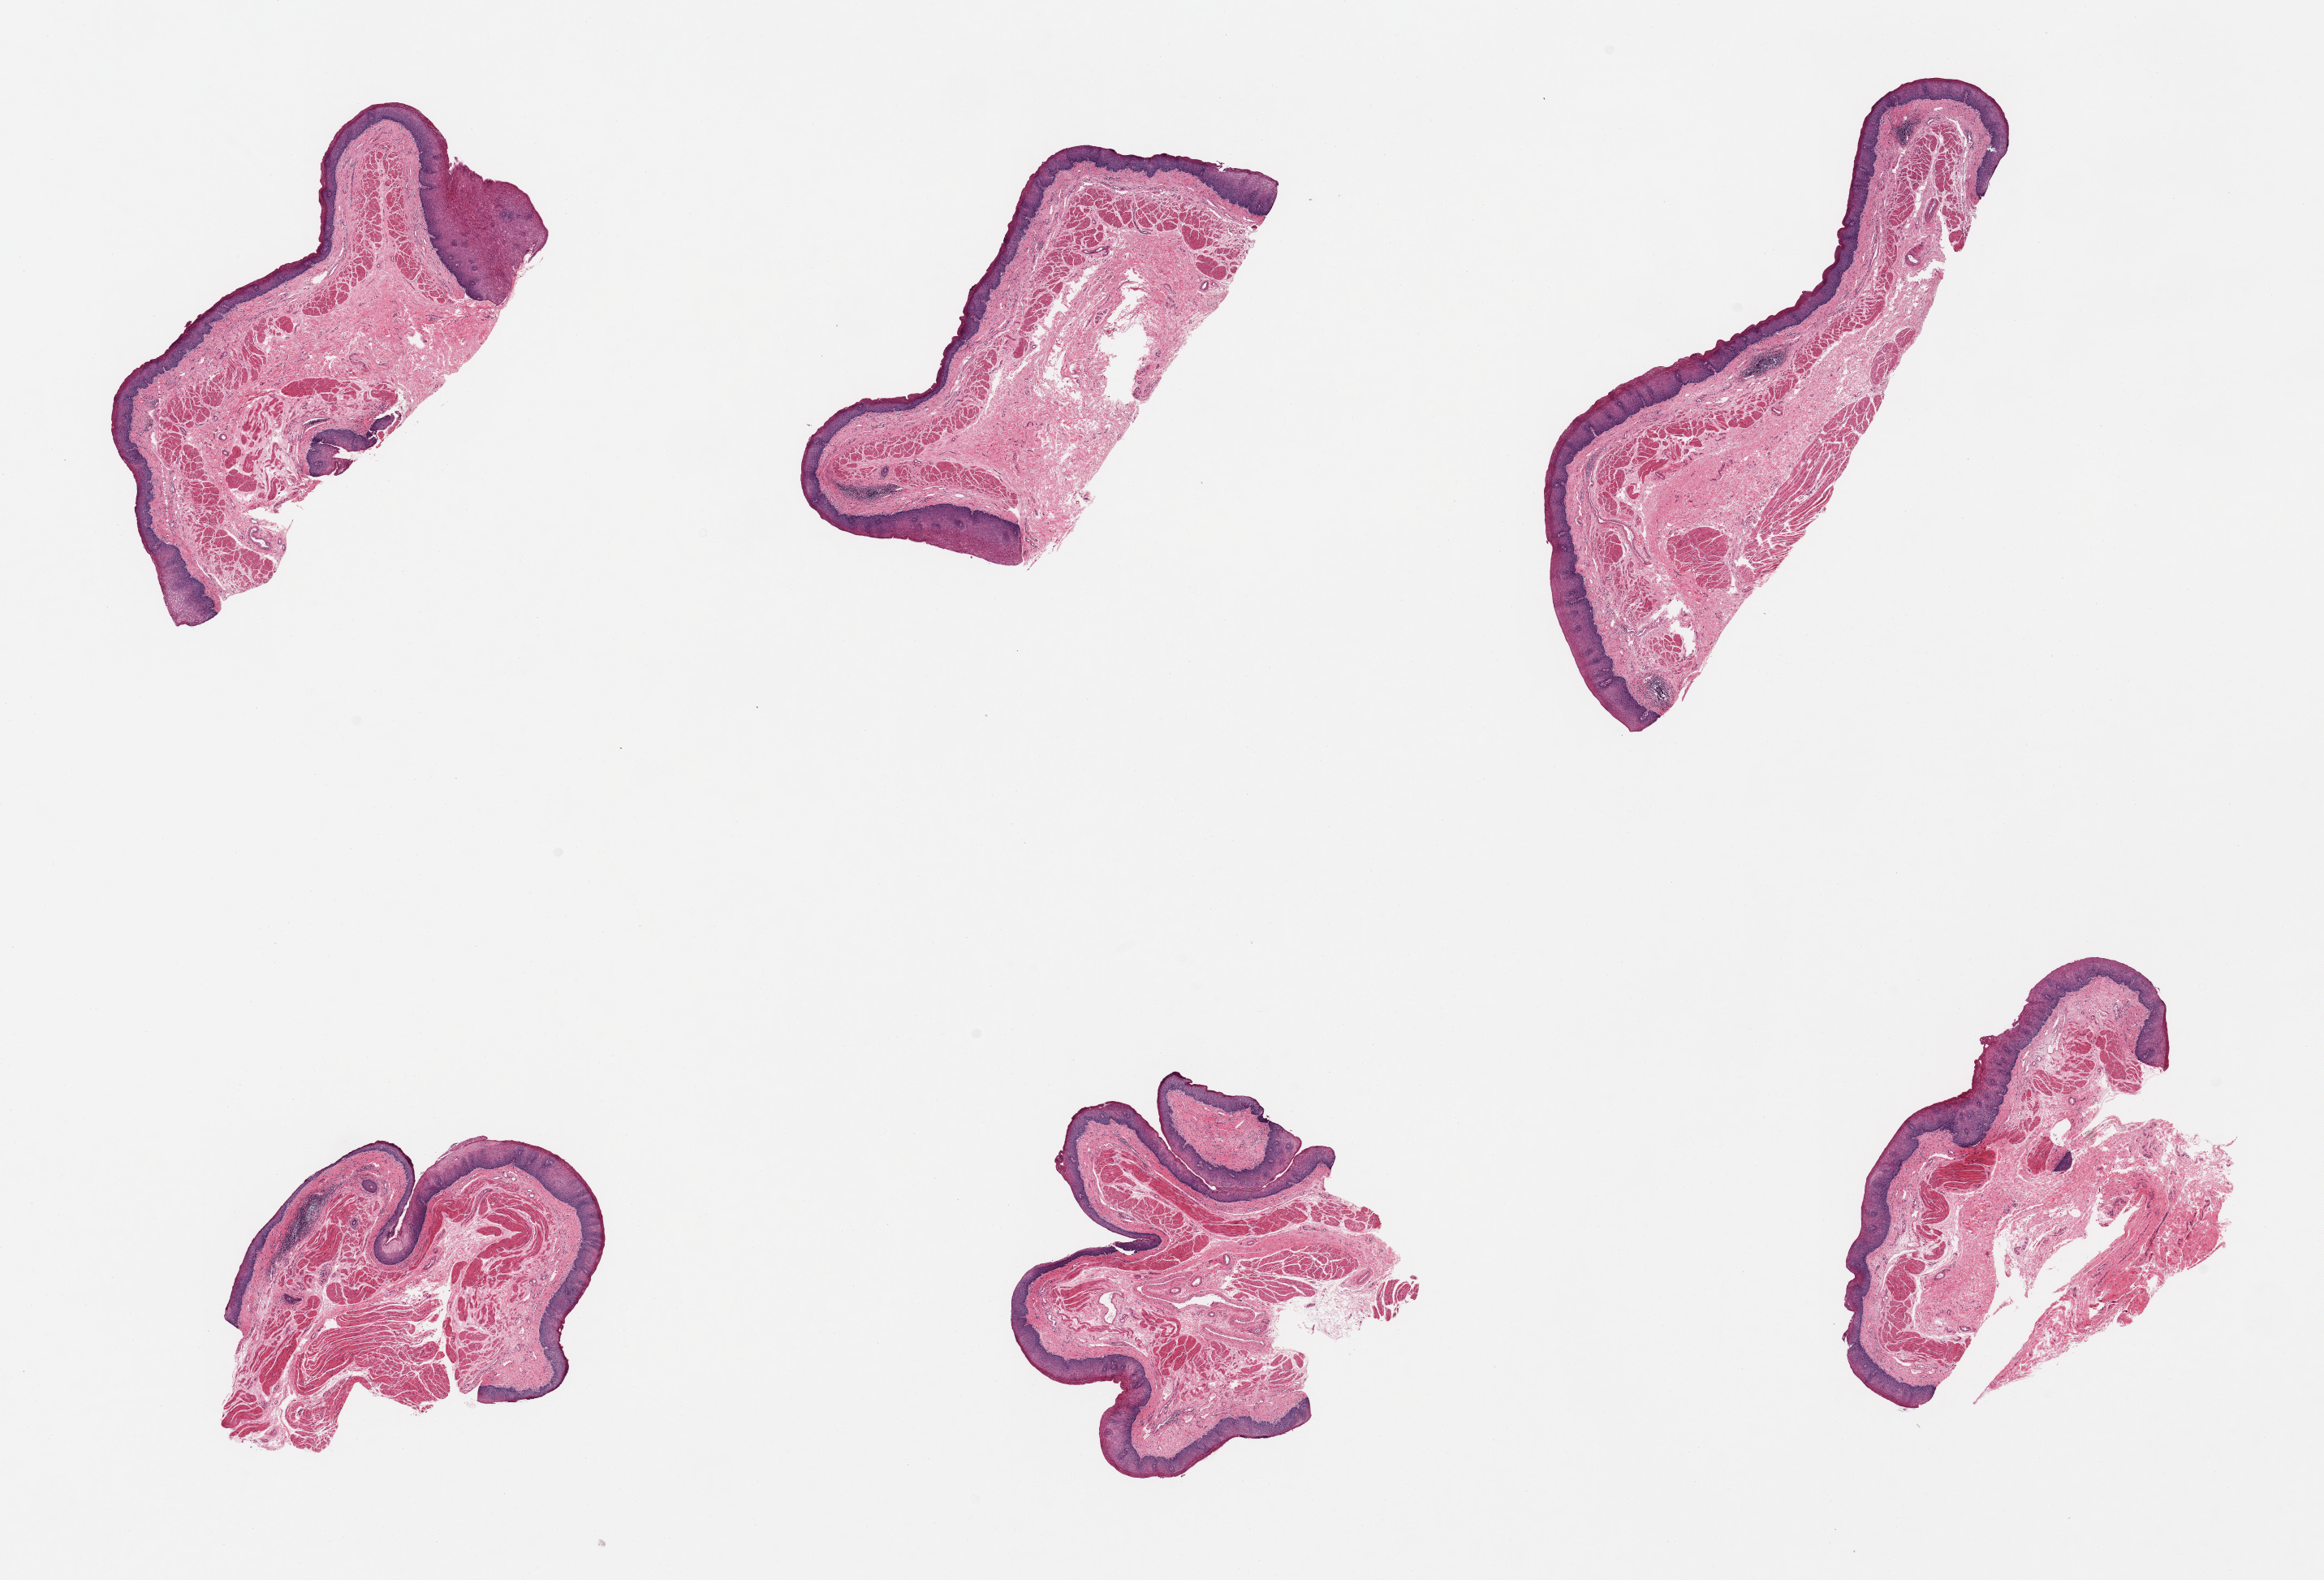
Haematoxylin and eosin whole-slide image, a low-resolution overview of the entire scanned area, about 22.6 x 15.4 mm; PAXgene-fixed, paraffin-embedded tissue; sampled site (target tissue): esophageal mucous membrane; donor tissue sample. Female donor.
Reviewer comment on this tissue sample: 6 pieces; well dissected.